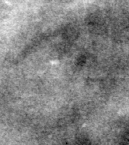
Cropped region of a digitized screen-film mammogram centred on a radiologist-marked abnormality; right breast; CC view; BI-RADS breast density category 3 (scale 1–4).
Calcifications, morphology punctate / pleomorphic, distribution clustered; BI-RADS assessment category 3; pathology result (as recorded, not read from the image): malignant.